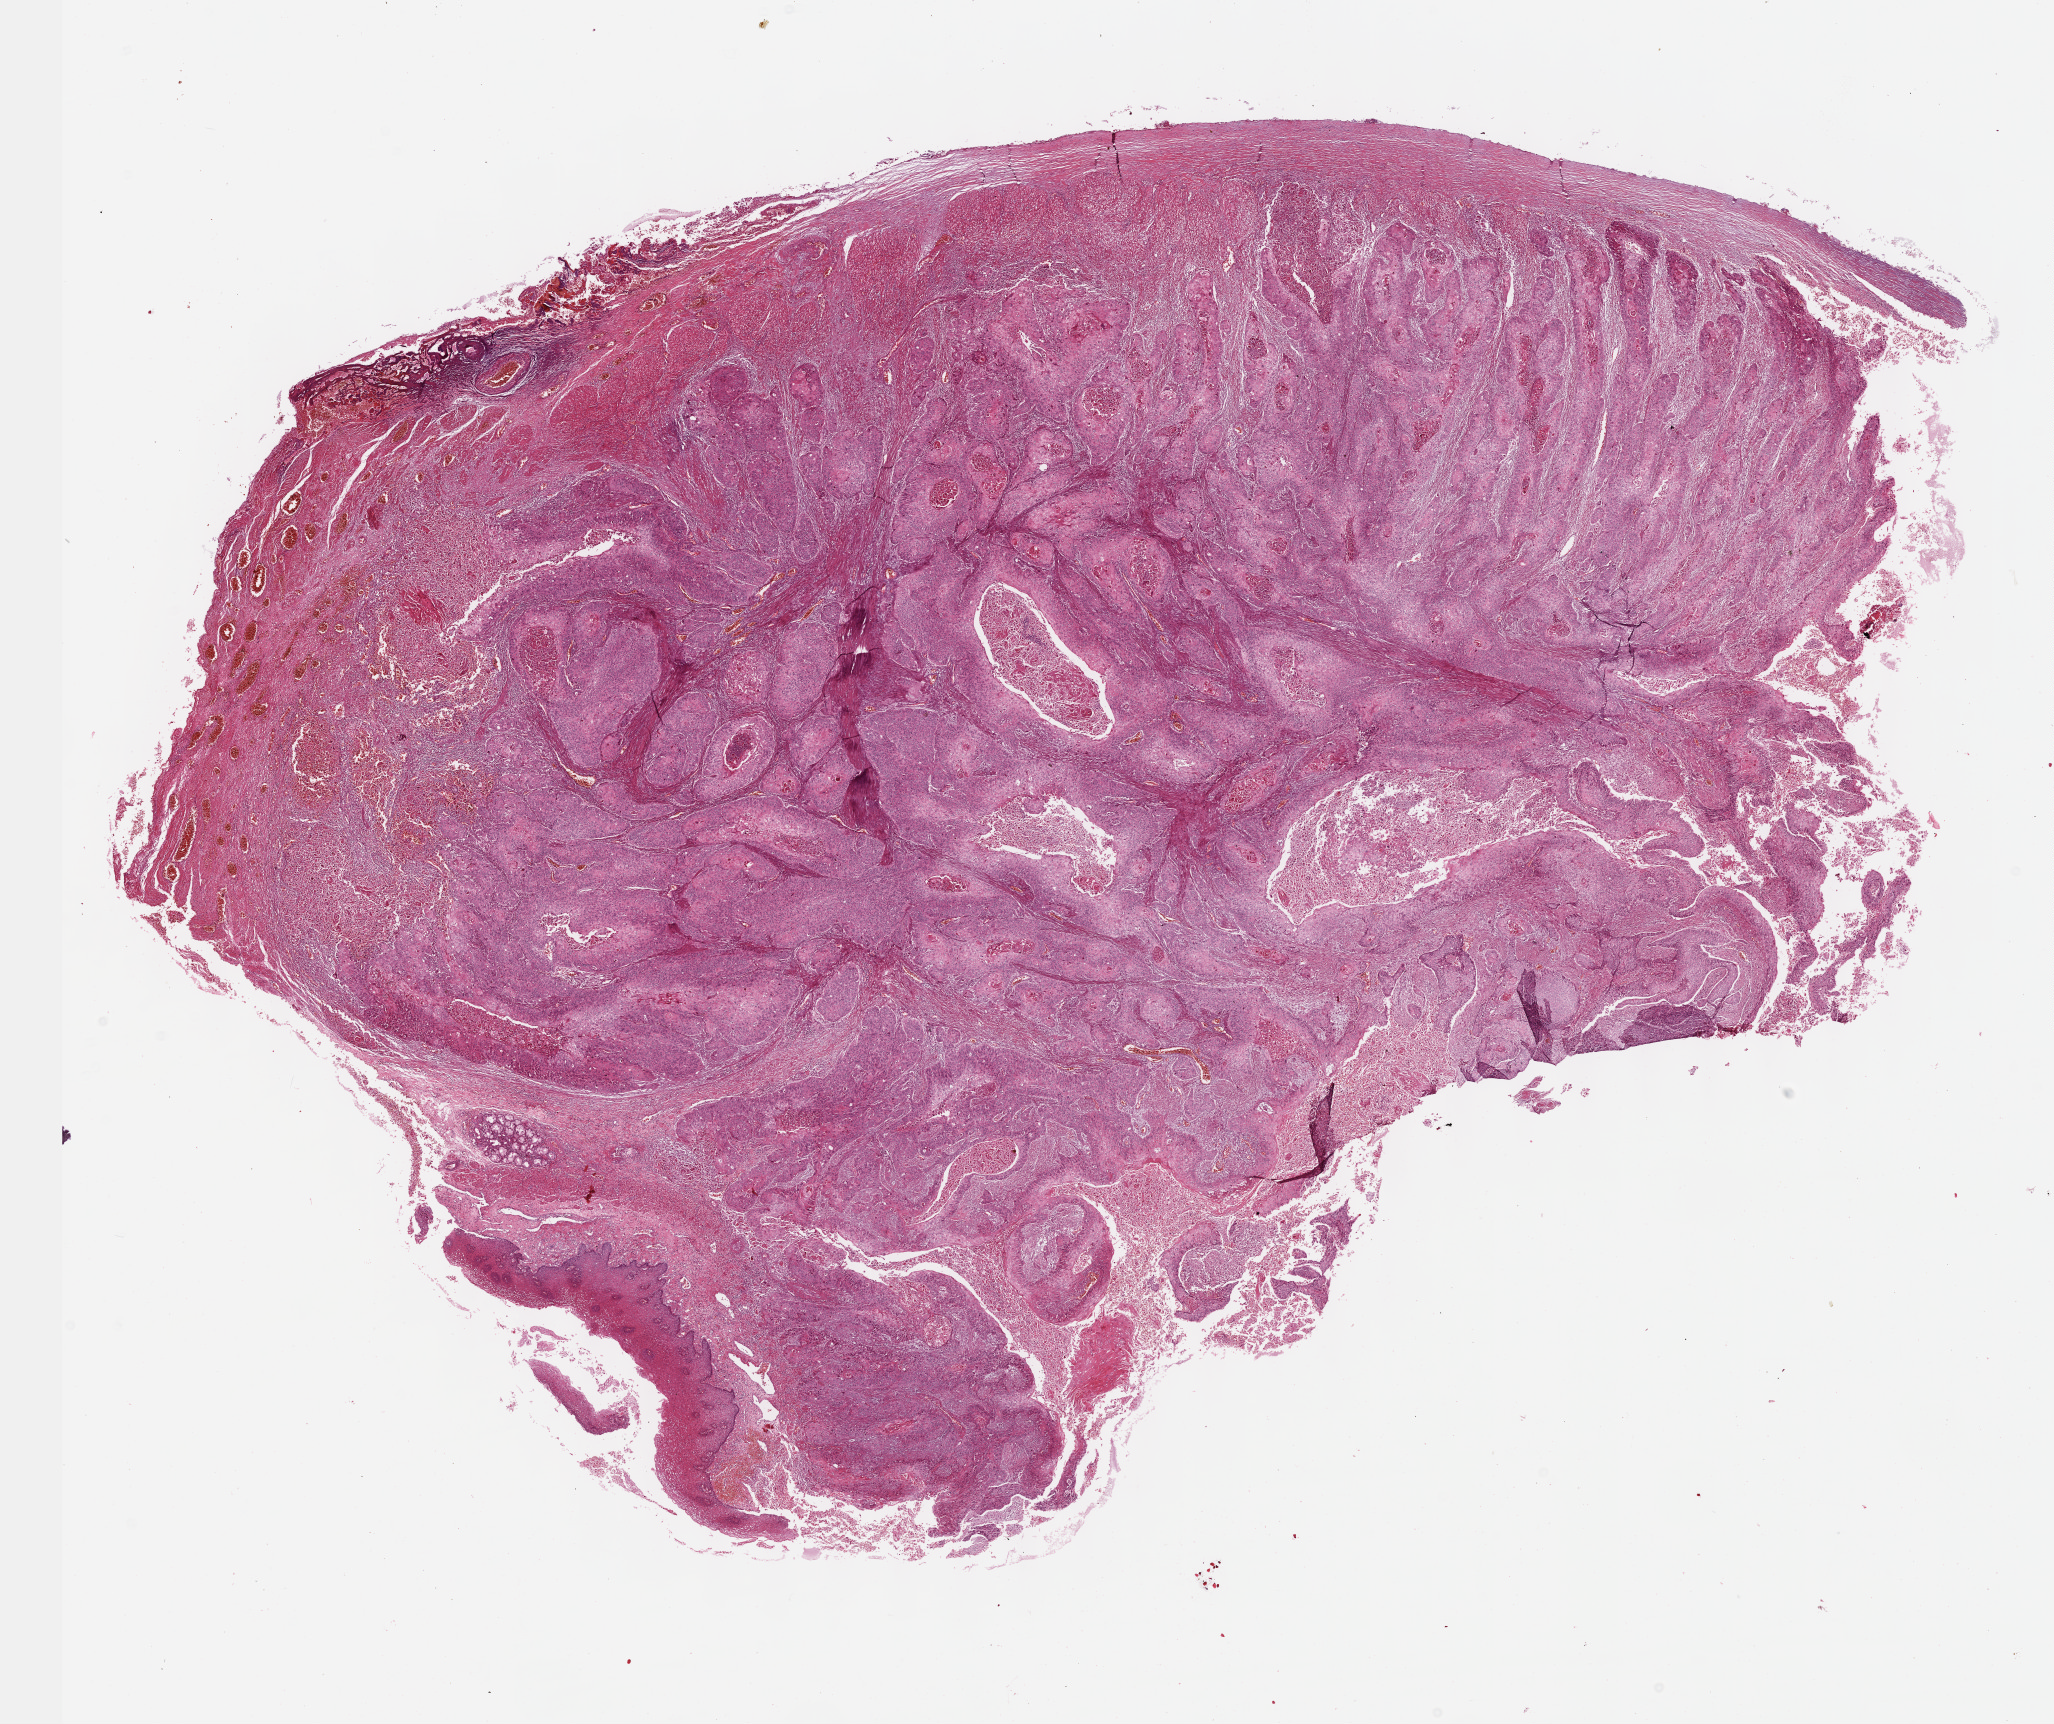
Digitized H&E-stained tissue section (whole slide) — low-resolution overview of the scanned area, about 16.6 x 13.9 mm. Formalin-fixed paraffin-embedded (FFPE) diagnostic section. Primary tumour sample from the esophagus. Male, age 52 years at initial diagnosis. Histologic grade: G2 (moderately differentiated).
AJCC pathologic stage: IIA (6th edition). Lymph nodes positive (case pathology): 0 of 2 examined. Histologic diagnosis: Squamous cell carcinoma, NOS.